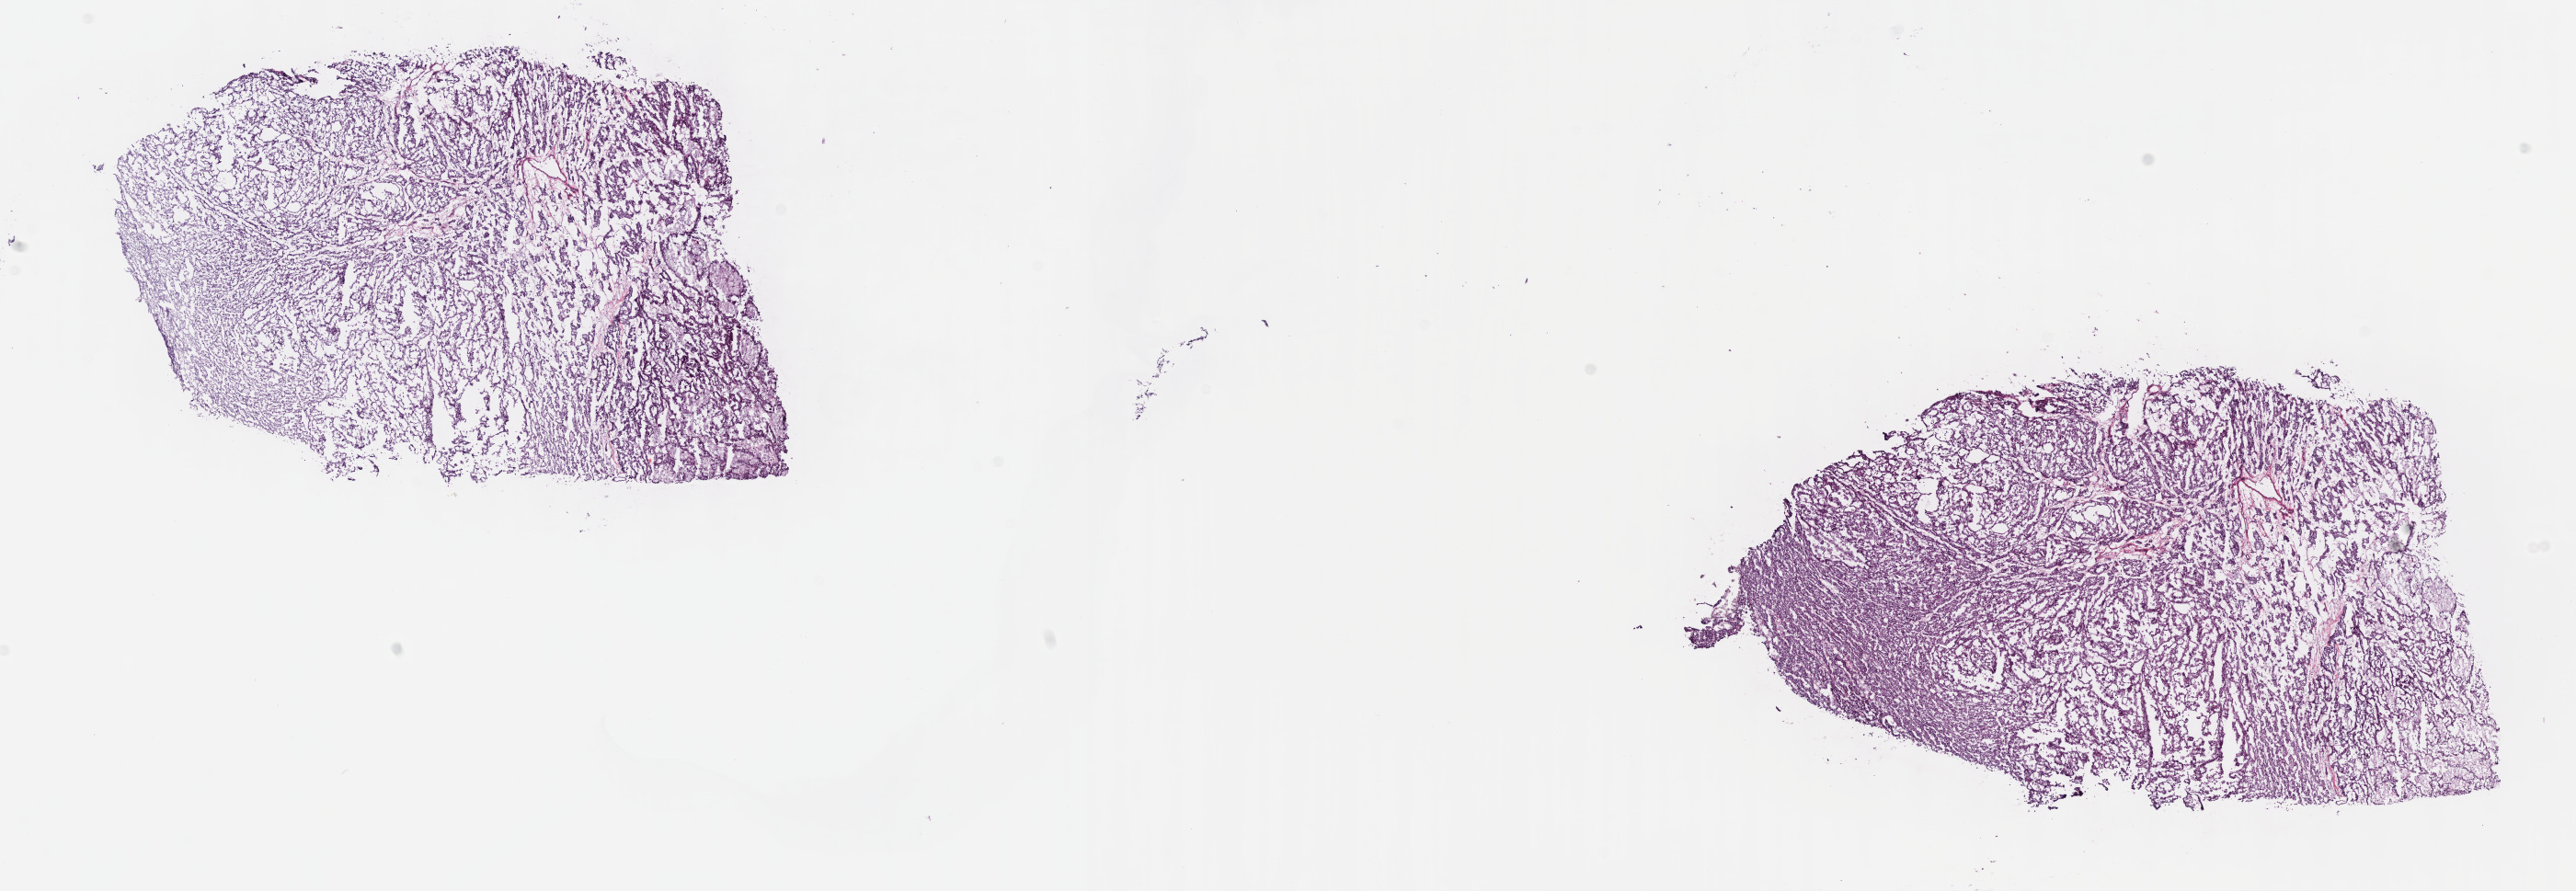
Whole-slide histology image, H&E, whole scanned area (about 22.7 x 7.8 mm, from a 40x scan) shown as a low-resolution overview. Frozen section. Sample: primary tumour, kidney. Male patient; age at initial diagnosis 63 years. Slide review estimates, as recorded: tumour cells 89%, tumour nuclei 90%, normal cells 0%, stromal cells 10%, necrosis 1%. Inflammatory infiltration, as recorded: lymphocyte infiltration 2%, monocyte infiltration 8%, neutrophil infiltration 0%.
AJCC pathologic stage: I (7th edition). TNM: T1b NX MX. Diagnosis: Papillary adenocarcinoma, NOS.